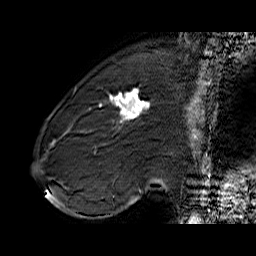
Breast MRI (dynamic contrast-enhanced), one sagittal slice. Position 19 of 60 along the scan axis. Dynamic contrast-enhanced series, time point 2 of 6 at this slice position (early post-contrast). 1.5 T. TE 6.4 ms, TR 32.9 ms. 4 mm slice thickness. 256 × 256 image matrix, field of view 200 × 200 mm. Female patient. Case-level facts recorded for this patient, not image findings: setting: breast cancer imaged before/during neoadjuvant chemotherapy; receptor status: HER2-positive.
Annotated regions visible in this slice (semi-automatic segmentation, software-assisted and operator-edited):
- analysis volume of interest (the breast-tissue region the enhancement analysis was run in; not a lesion): box from (x=71, y=80) to (x=155, y=146) px
- tumour enhancement mask (voxels above the 100 % enhancement threshold inside the analysis volume of interest): (x=100, y=88)–(x=150, y=122)